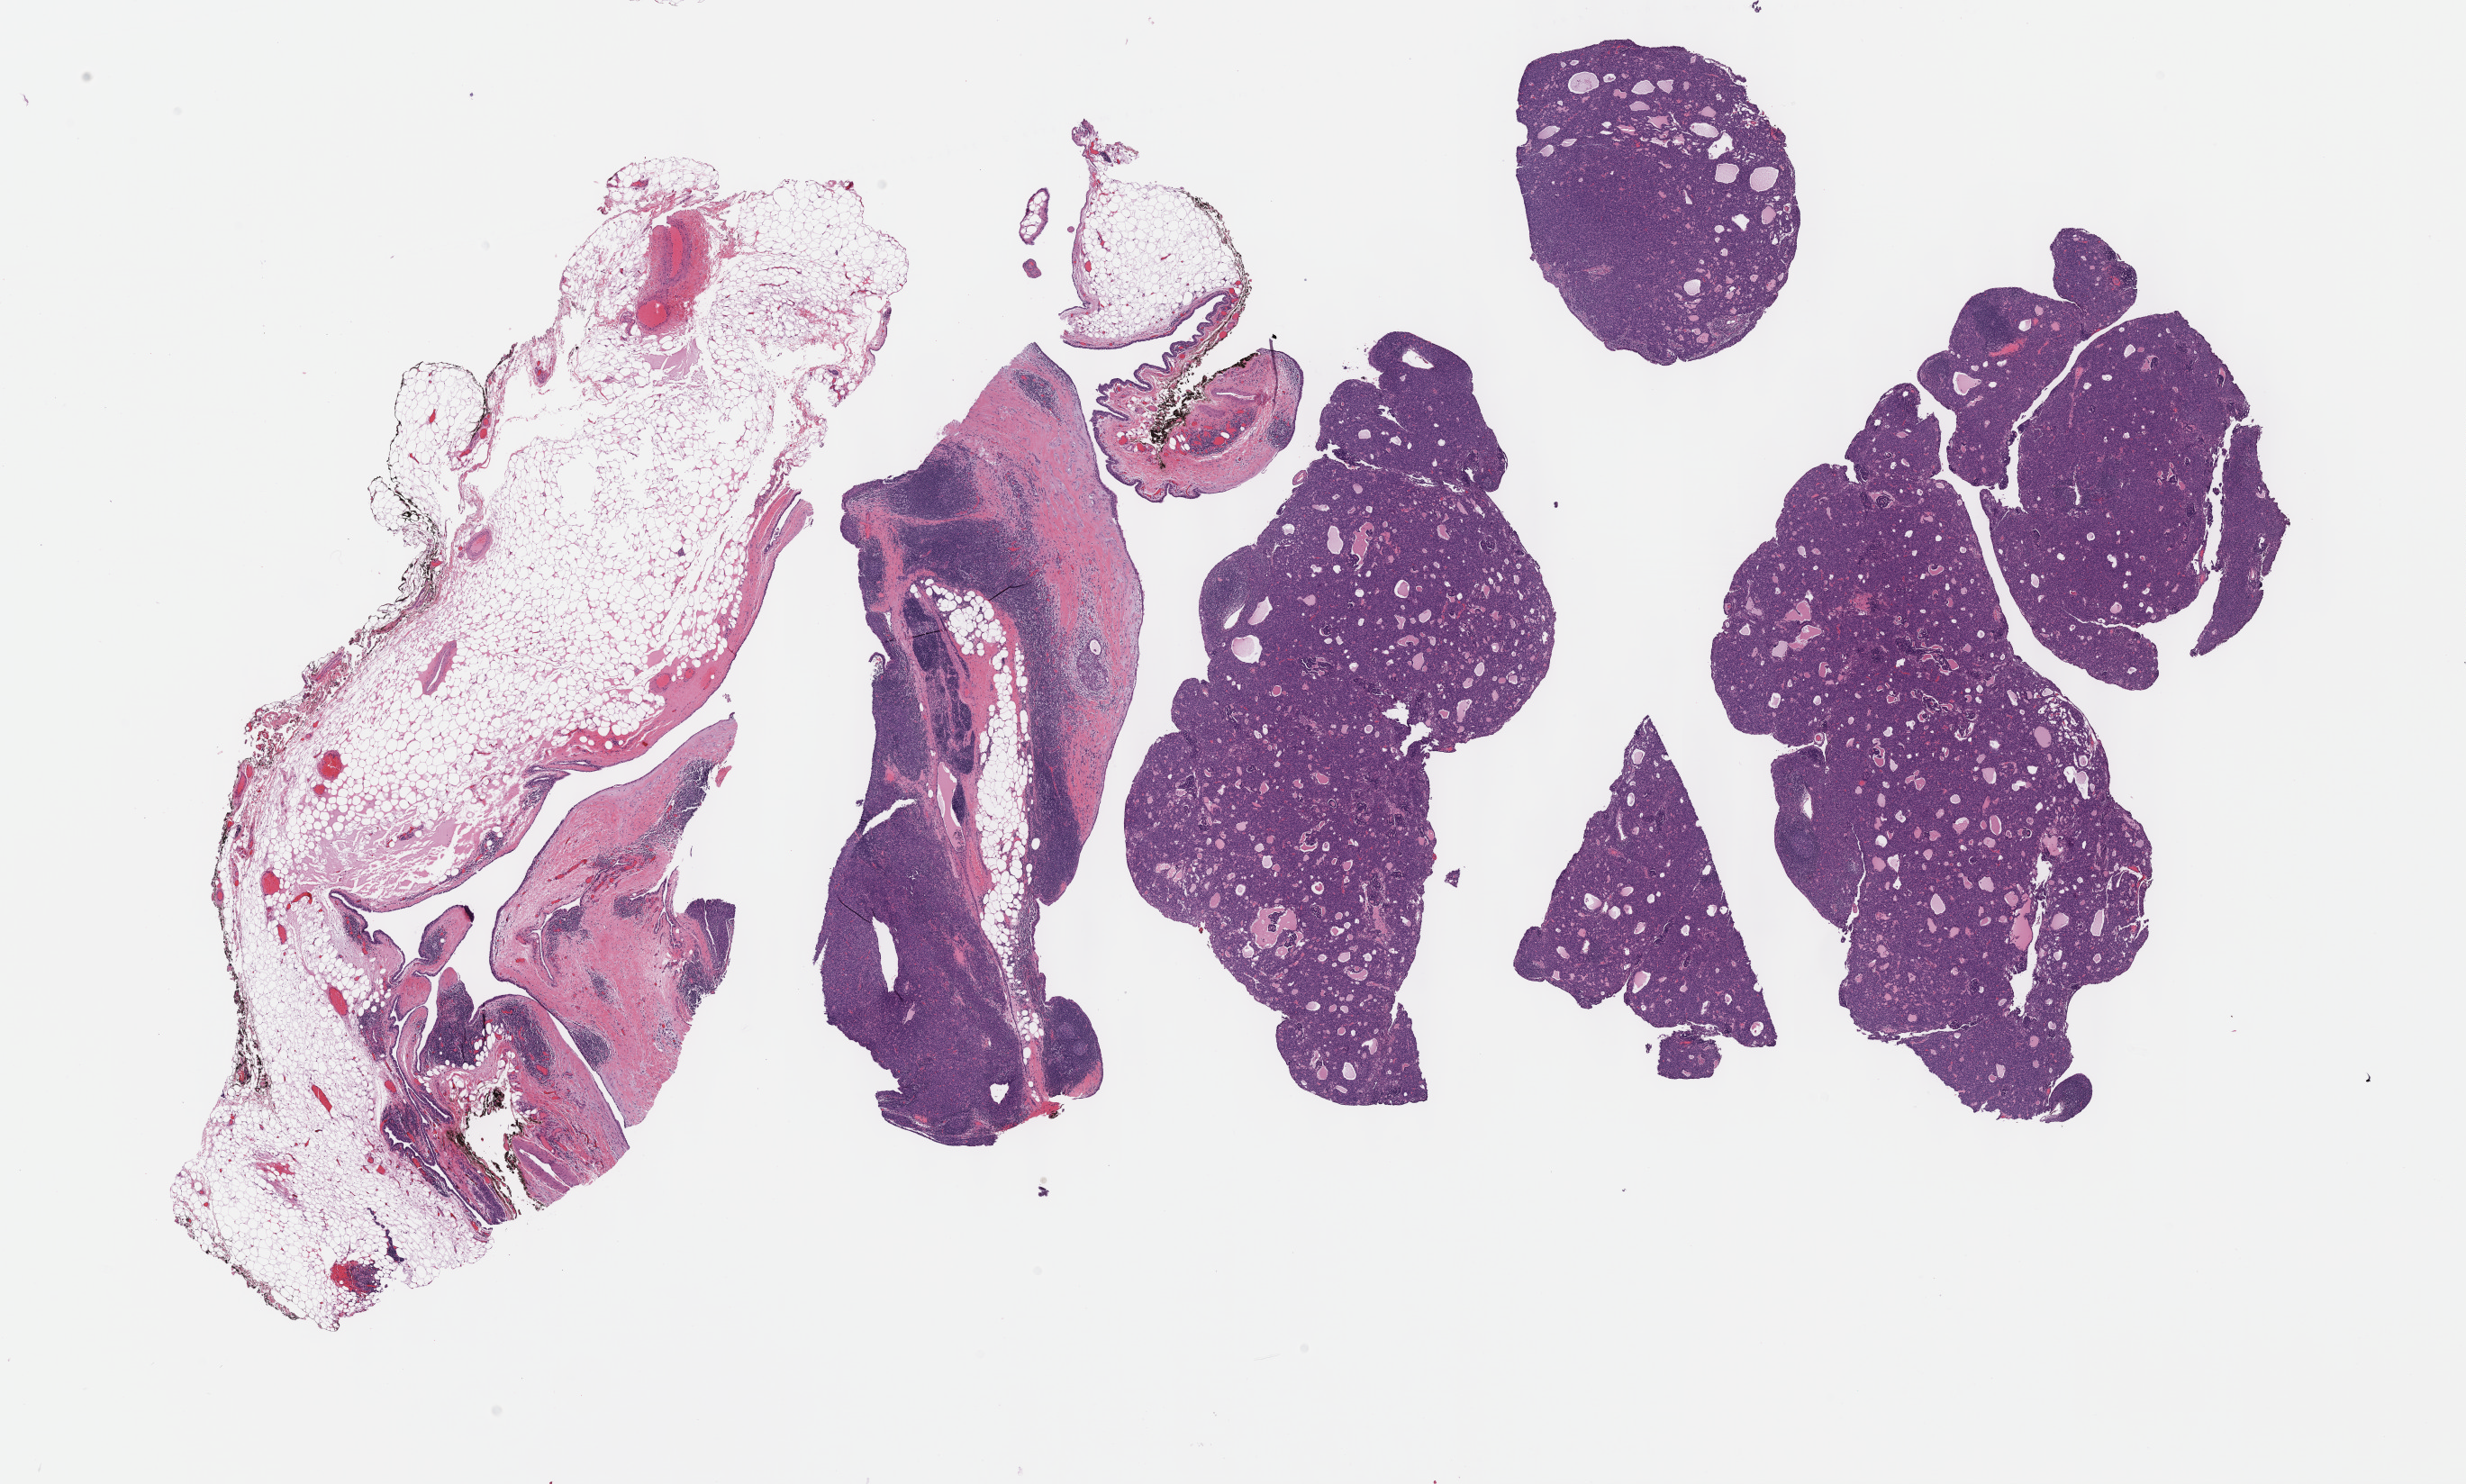
Hematoxylin and eosin (H&E) stained whole-slide image — a low-resolution overview of the entire scanned area, about 22.1 x 13.3 mm, formalin-fixed paraffin-embedded (FFPE) diagnostic section, sample: primary tumour, thymus. Patient: male, age at initial diagnosis 61 years.
* diagnosis: Thymoma, type AB, malignant